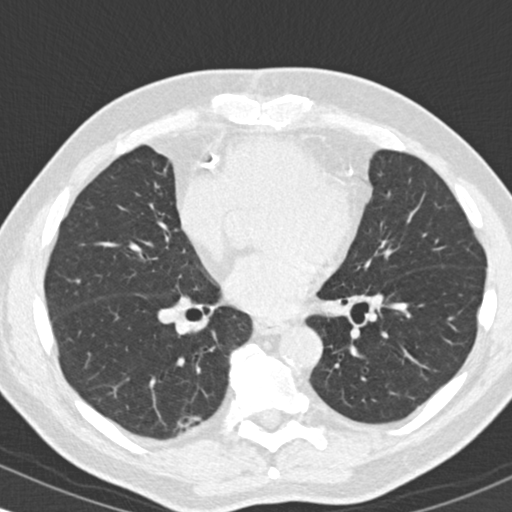
Axial slice from a low-dose chest CT screening exam, second annual screen, lung window (W 1500 / L -600 HU), 512 × 512 image matrix, field of view 318 × 318 mm. Male, age 68 years at enrolment. Former smoker at enrolment.
Expert-annotated lung lesion, box from (x=165, y=403) to (x=219, y=445) px. The screening reader recorded 2 non-calcified nodules or masses ≥4 mm on this exam; which of them this box marks is not recorded. Lung cancer was diagnosed 476 days after this screen (after the third annual screen): adenosquamous carcinoma, right lower lobe, moderately differentiated (G2), stage IB (AJCC 6th edition), 31 mm at pathology.